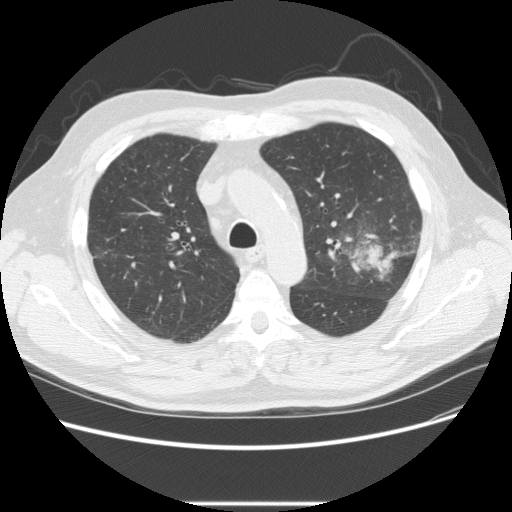
Chest CT (low-dose screening protocol), one axial image; first (baseline) screen; lung window (W 1500 / L -600 HU); 2.5 mm slice thickness; slice 70 of 233 in the series. Male, age 73 years at enrolment.
Expert-annotated lung lesion, bounding box [x1, y1, x2, y2] px = [332, 215, 420, 288]. The screening reader recorded 2 non-calcified nodules or masses ≥4 mm on this exam (left upper lobe, right upper lobe); which of them this box marks is not recorded. Participant outcome: lung cancer diagnosed 11 days after this screen — bronchiolo-alveolar adenocarcinoma, NOS, other location, well differentiated (G1), stage IV (AJCC 6th edition).